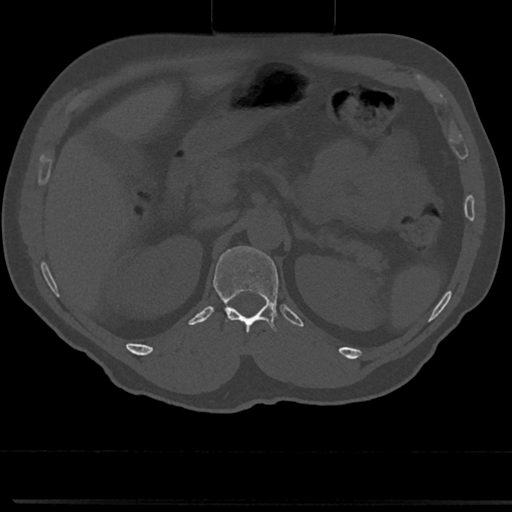
CT including the spine, one axial slice; slice 140 of 817 in the series (ordered by position); bone window (W 1800 / L 400 HU); 0.5 mm slice thickness; 512 × 512 image matrix, field of view 355 × 355 mm. Male patient, age 61 years. Case-level facts recorded for this patient, not image findings: primary cancer: prostate.
Structures marked on this image (semi-automatically segmented with operator editing):
- T12 vertebra: box from (x=211, y=253) to (x=282, y=356) px